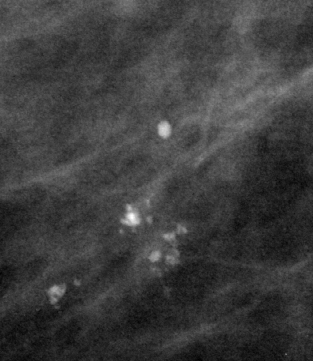
Cropped region of a digitized screen-film mammogram centred on a radiologist-marked abnormality, right breast, MLO view, BI-RADS breast density category 2 (scale 1–4).
Marked abnormality: calcifications, morphology pleomorphic, distribution clustered; BI-RADS assessment category 2; subtlety rating 4 on a 1 (subtle) to 5 (obvious) scale; benign; no additional work-up was recommended (benign without callback).